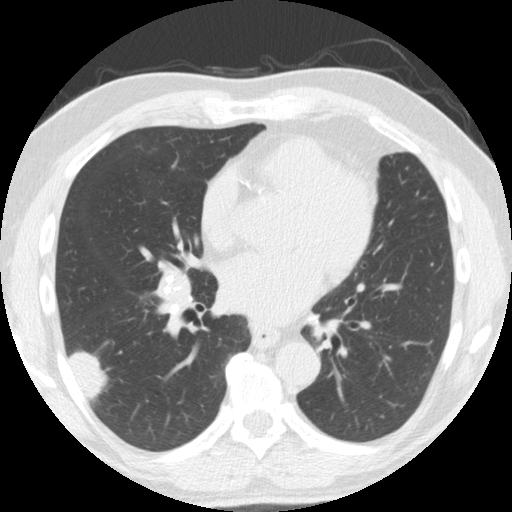
Chest CT (low-dose screening protocol), one axial image; second annual screen; lung window (W 1500 / L -600 HU); 2.5 mm slice thickness; 120 kVp; 512 × 512 image matrix, field of view 341 × 341 mm. Male, age 61 years at enrolment. Former smoker at enrolment.
Expert reader's lesion annotation, bounding box (x1, y1, x2, y2) in pixels: (50, 326, 117, 401). Screening reader's record for this exam (one nodule recorded; not confirmed to be the boxed lesion): non-calcified nodule or mass ≥4 mm, right lower lobe, 33 × 19 mm, smooth margins, soft tissue attenuation, pre-existing on the prior screen: yes; interval growth: yes. Participant outcome: lung cancer diagnosed 30 days after this screen — adenosquamous carcinoma, right lower lobe, poorly differentiated (G3), stage IV (AJCC 6th edition), 45 mm at pathology.